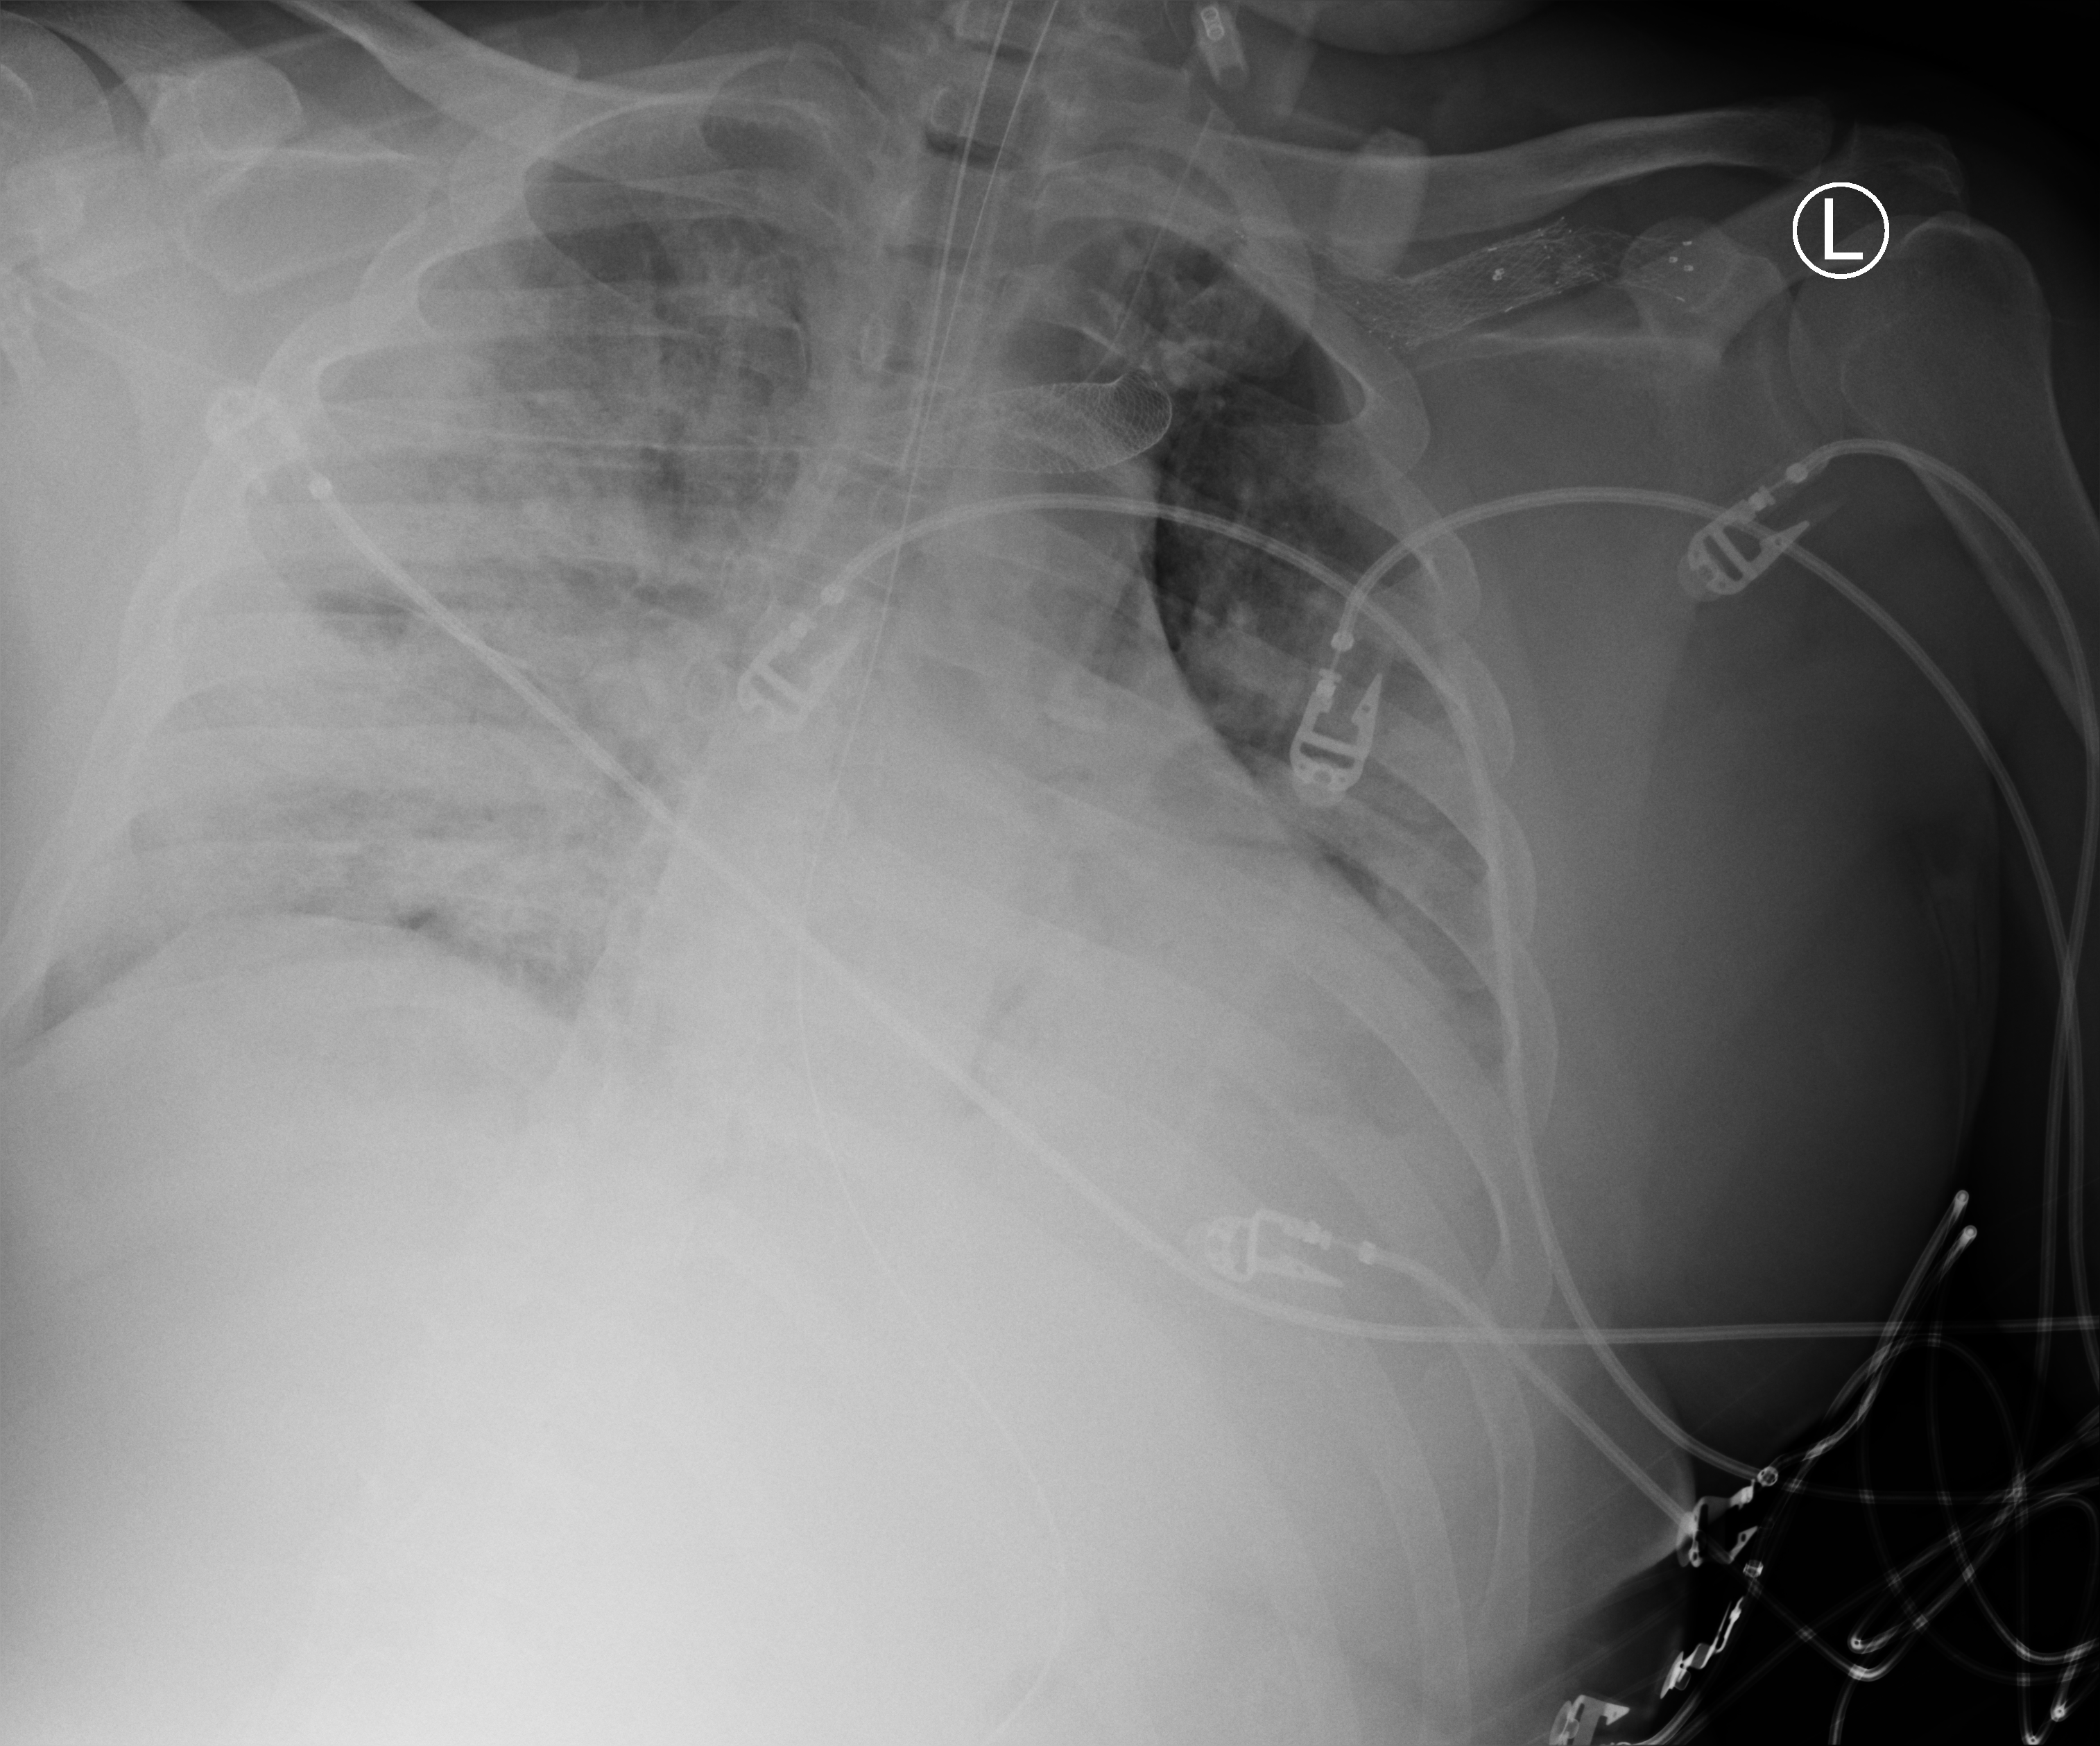
Bedside chest radiograph (computed radiography); anteroposterior (AP) projection. Patient hospitalised with COVID-19; male, aged 18–59 years.
From the hospital-stay record, not from the radiograph (when in the stay this image was taken is not recorded):
- admitted to intensive care during this hospital stay: yes